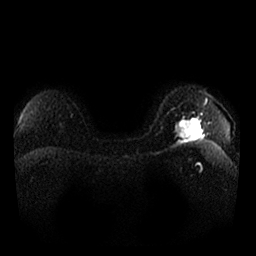
Breast MRI, one axial slice. Position 17 of 25 along the scan axis. Diffusion-weighted series; image 2 of 4 stored at this slice position (different b-values; order by instance number). 1.5 T. 256 × 256 image matrix, field of view 340 × 340 mm. Female patient.
Annotated regions visible in this slice (expert manual segmentation):
- tumour on diffusion-weighted imaging: bounding box [x1, y1, x2, y2] px = [174, 117, 202, 141]